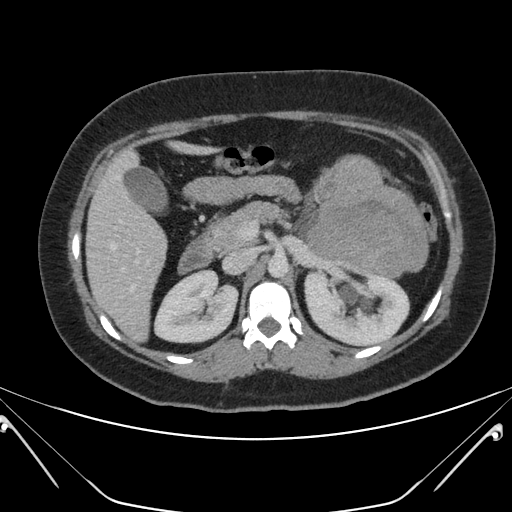
Contrast-enhanced abdominal CT, one axial slice; slice 121 of 168 in the series (ordered by position); 120 kVp; intravenous contrast given; soft-tissue window (W 400 / L 40 HU); 3 mm slice thickness; 512 × 512 image matrix, field of view 394 × 394 mm. Female patient, age 26 years. Case-level facts recorded for this patient, not image findings: diagnosis: adrenocortical carcinoma; tumour side: left adrenal; tumour size at pathology: 28 cm; Ki-67 index: 20 %; stage (as recorded): 2.
Structures marked on this image (semi-automatic segmentation, software-assisted and operator-edited):
- mass: bounding box <307,157,426,274> (left, top, right, bottom; pixels)